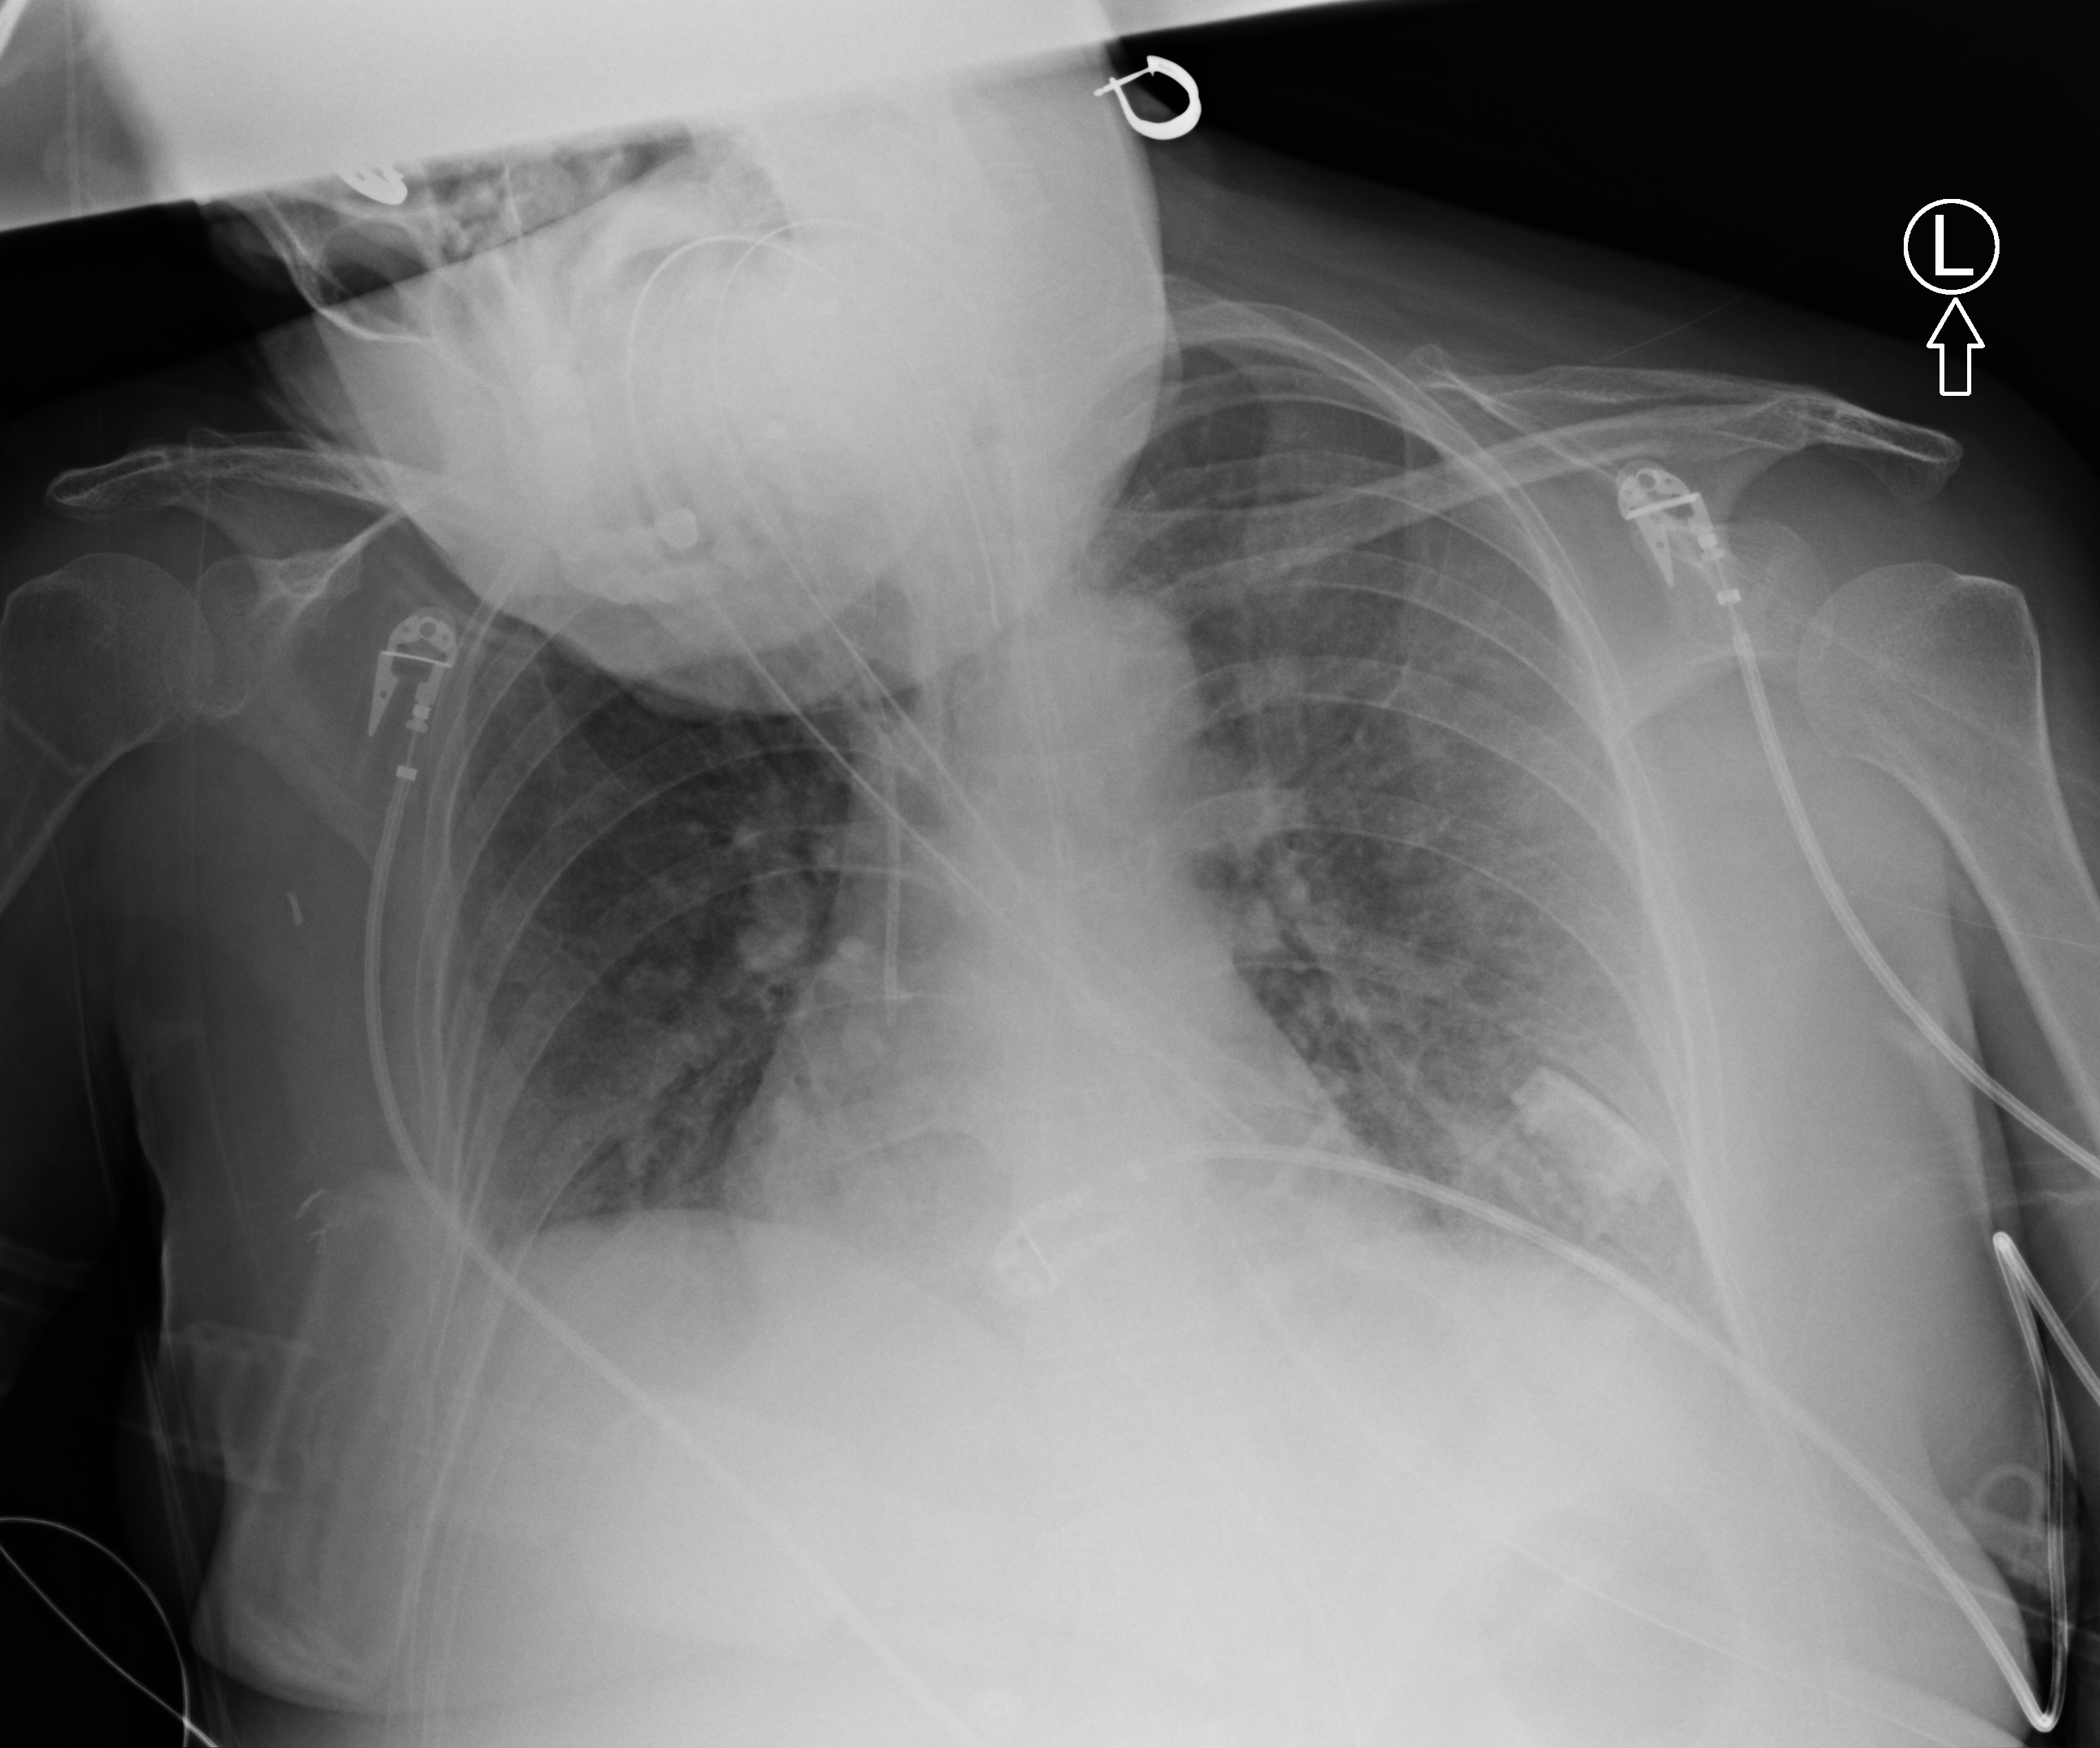
Chest X-ray (portable), anteroposterior (AP) projection. Female patient hospitalised with COVID-19, age 18–59 years.
From the hospital-stay record, not from the radiograph (when in the stay this image was taken is not recorded):
- admitted to intensive care during this hospital stay: no
- COPD (admission record): no
- chronic kidney disease (admission record): no